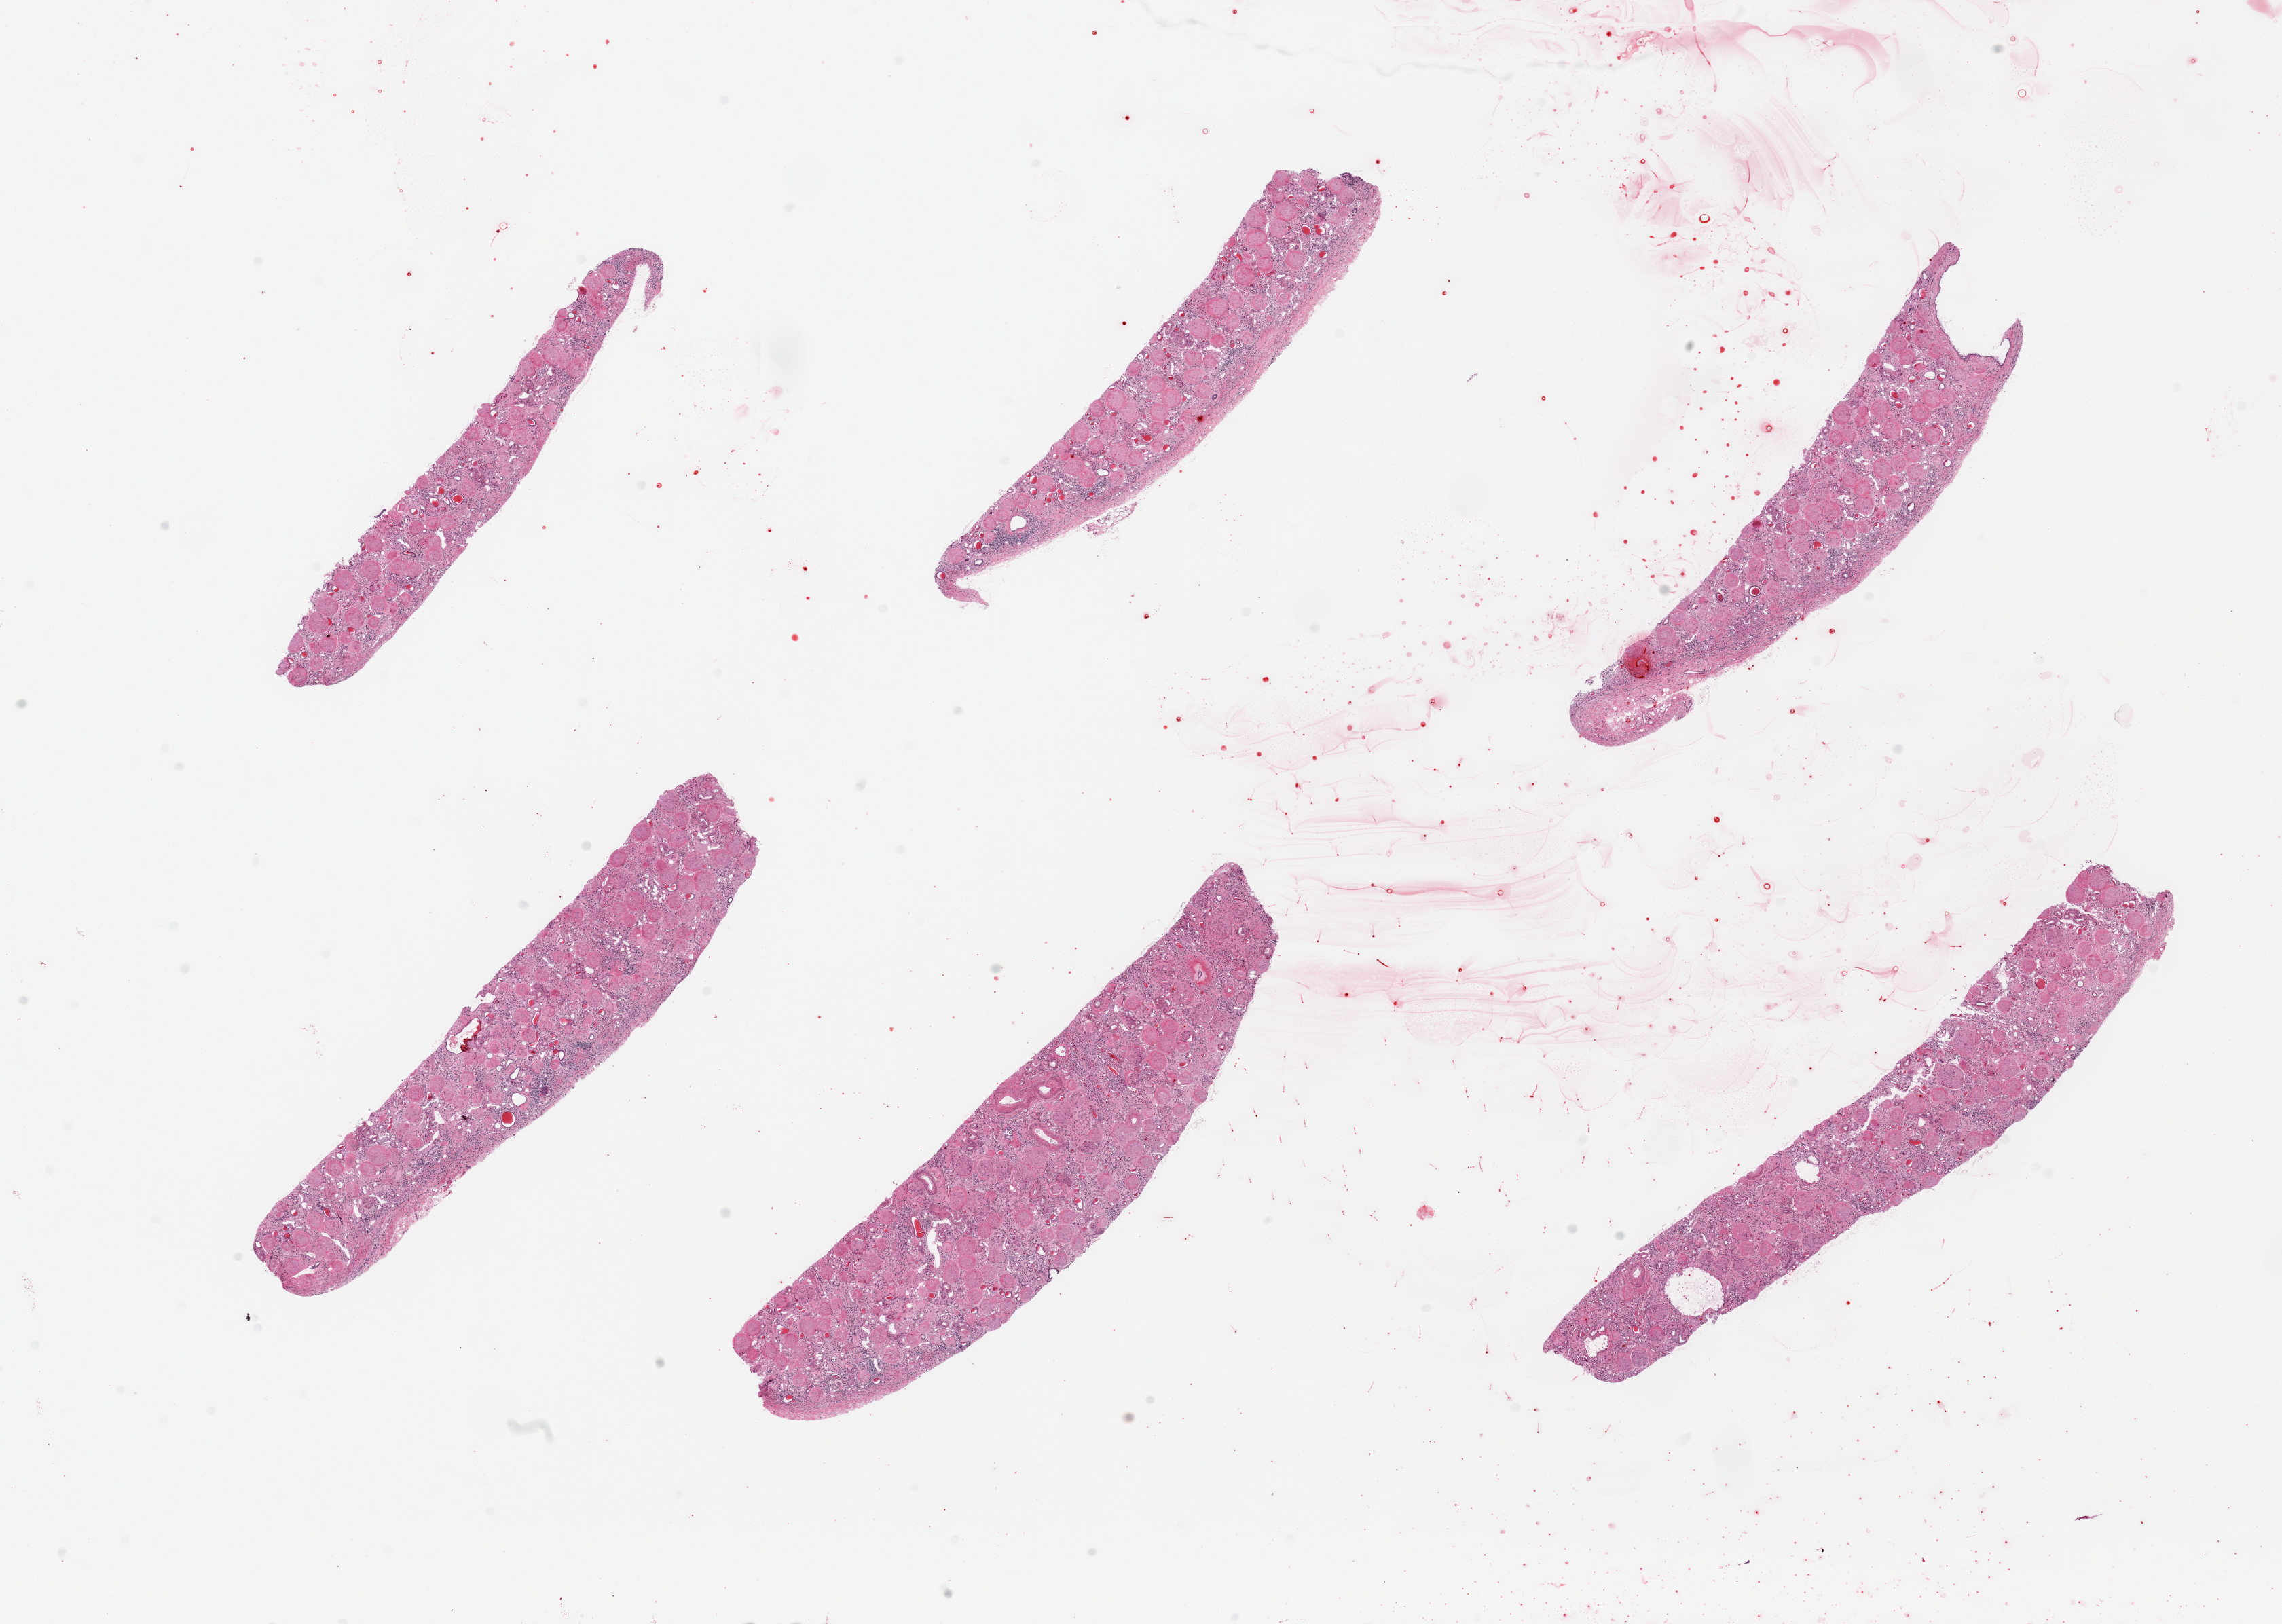
Haematoxylin and eosin whole-slide image, brightfield — shown as a low-resolution overview of the whole scanned area (about 26.6 x 18.9 mm). PAXgene-fixed, paraffin-embedded tissue. Sampled site (target tissue): renal cortex. Donor tissue sample. Donor: male.
Review note (as recorded): 6 pieces, glomeruli present, diffuse waxy infiltrative process s/o amyloid.